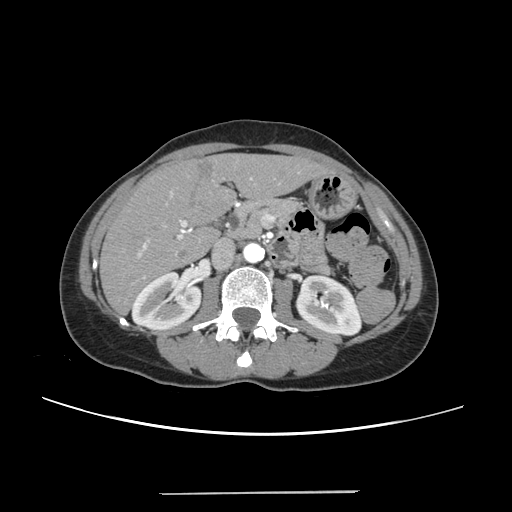
Contrast-enhanced abdominal CT, one axial slice; slice 116 of 240 in the series (ordered by position); 120 kVp; intravenous contrast given; soft-tissue window (W 400 / L 40 HU); 1.25 mm slice thickness; 512 × 512 image matrix. Female patient, age 60 years. Case-level facts recorded for this patient, not image findings: diagnosis: colorectal cancer liver metastases, imaged before liver resection; multiple liver metastases: no; largest metastasis: 1.5 cm; disease in both lobes: no.
Annotated regions visible in this slice (expert manual segmentation):
- liver: bounding box [x1, y1, x2, y2] px = [101, 154, 328, 312]
- planned liver remnant (the part of the liver to remain after resection): [101, 155, 328, 312]
- portal vein (with intrahepatic branches): [138, 178, 252, 277]
- liver metastasis: [196, 163, 214, 181]